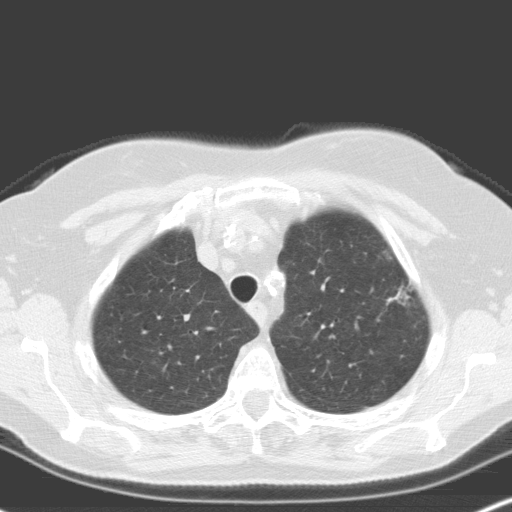
Low-dose screening chest CT, one axial slice; position 136 of 160 along the scan axis; 120 kVp; lung window (W 1500 / L -600 HU); 3.2 mm slice thickness; 512 × 512 image matrix.
Annotated regions visible in this slice (manually delineated by an expert):
- lesion 2 (nodule): box from (x=390, y=294) to (x=408, y=302) px